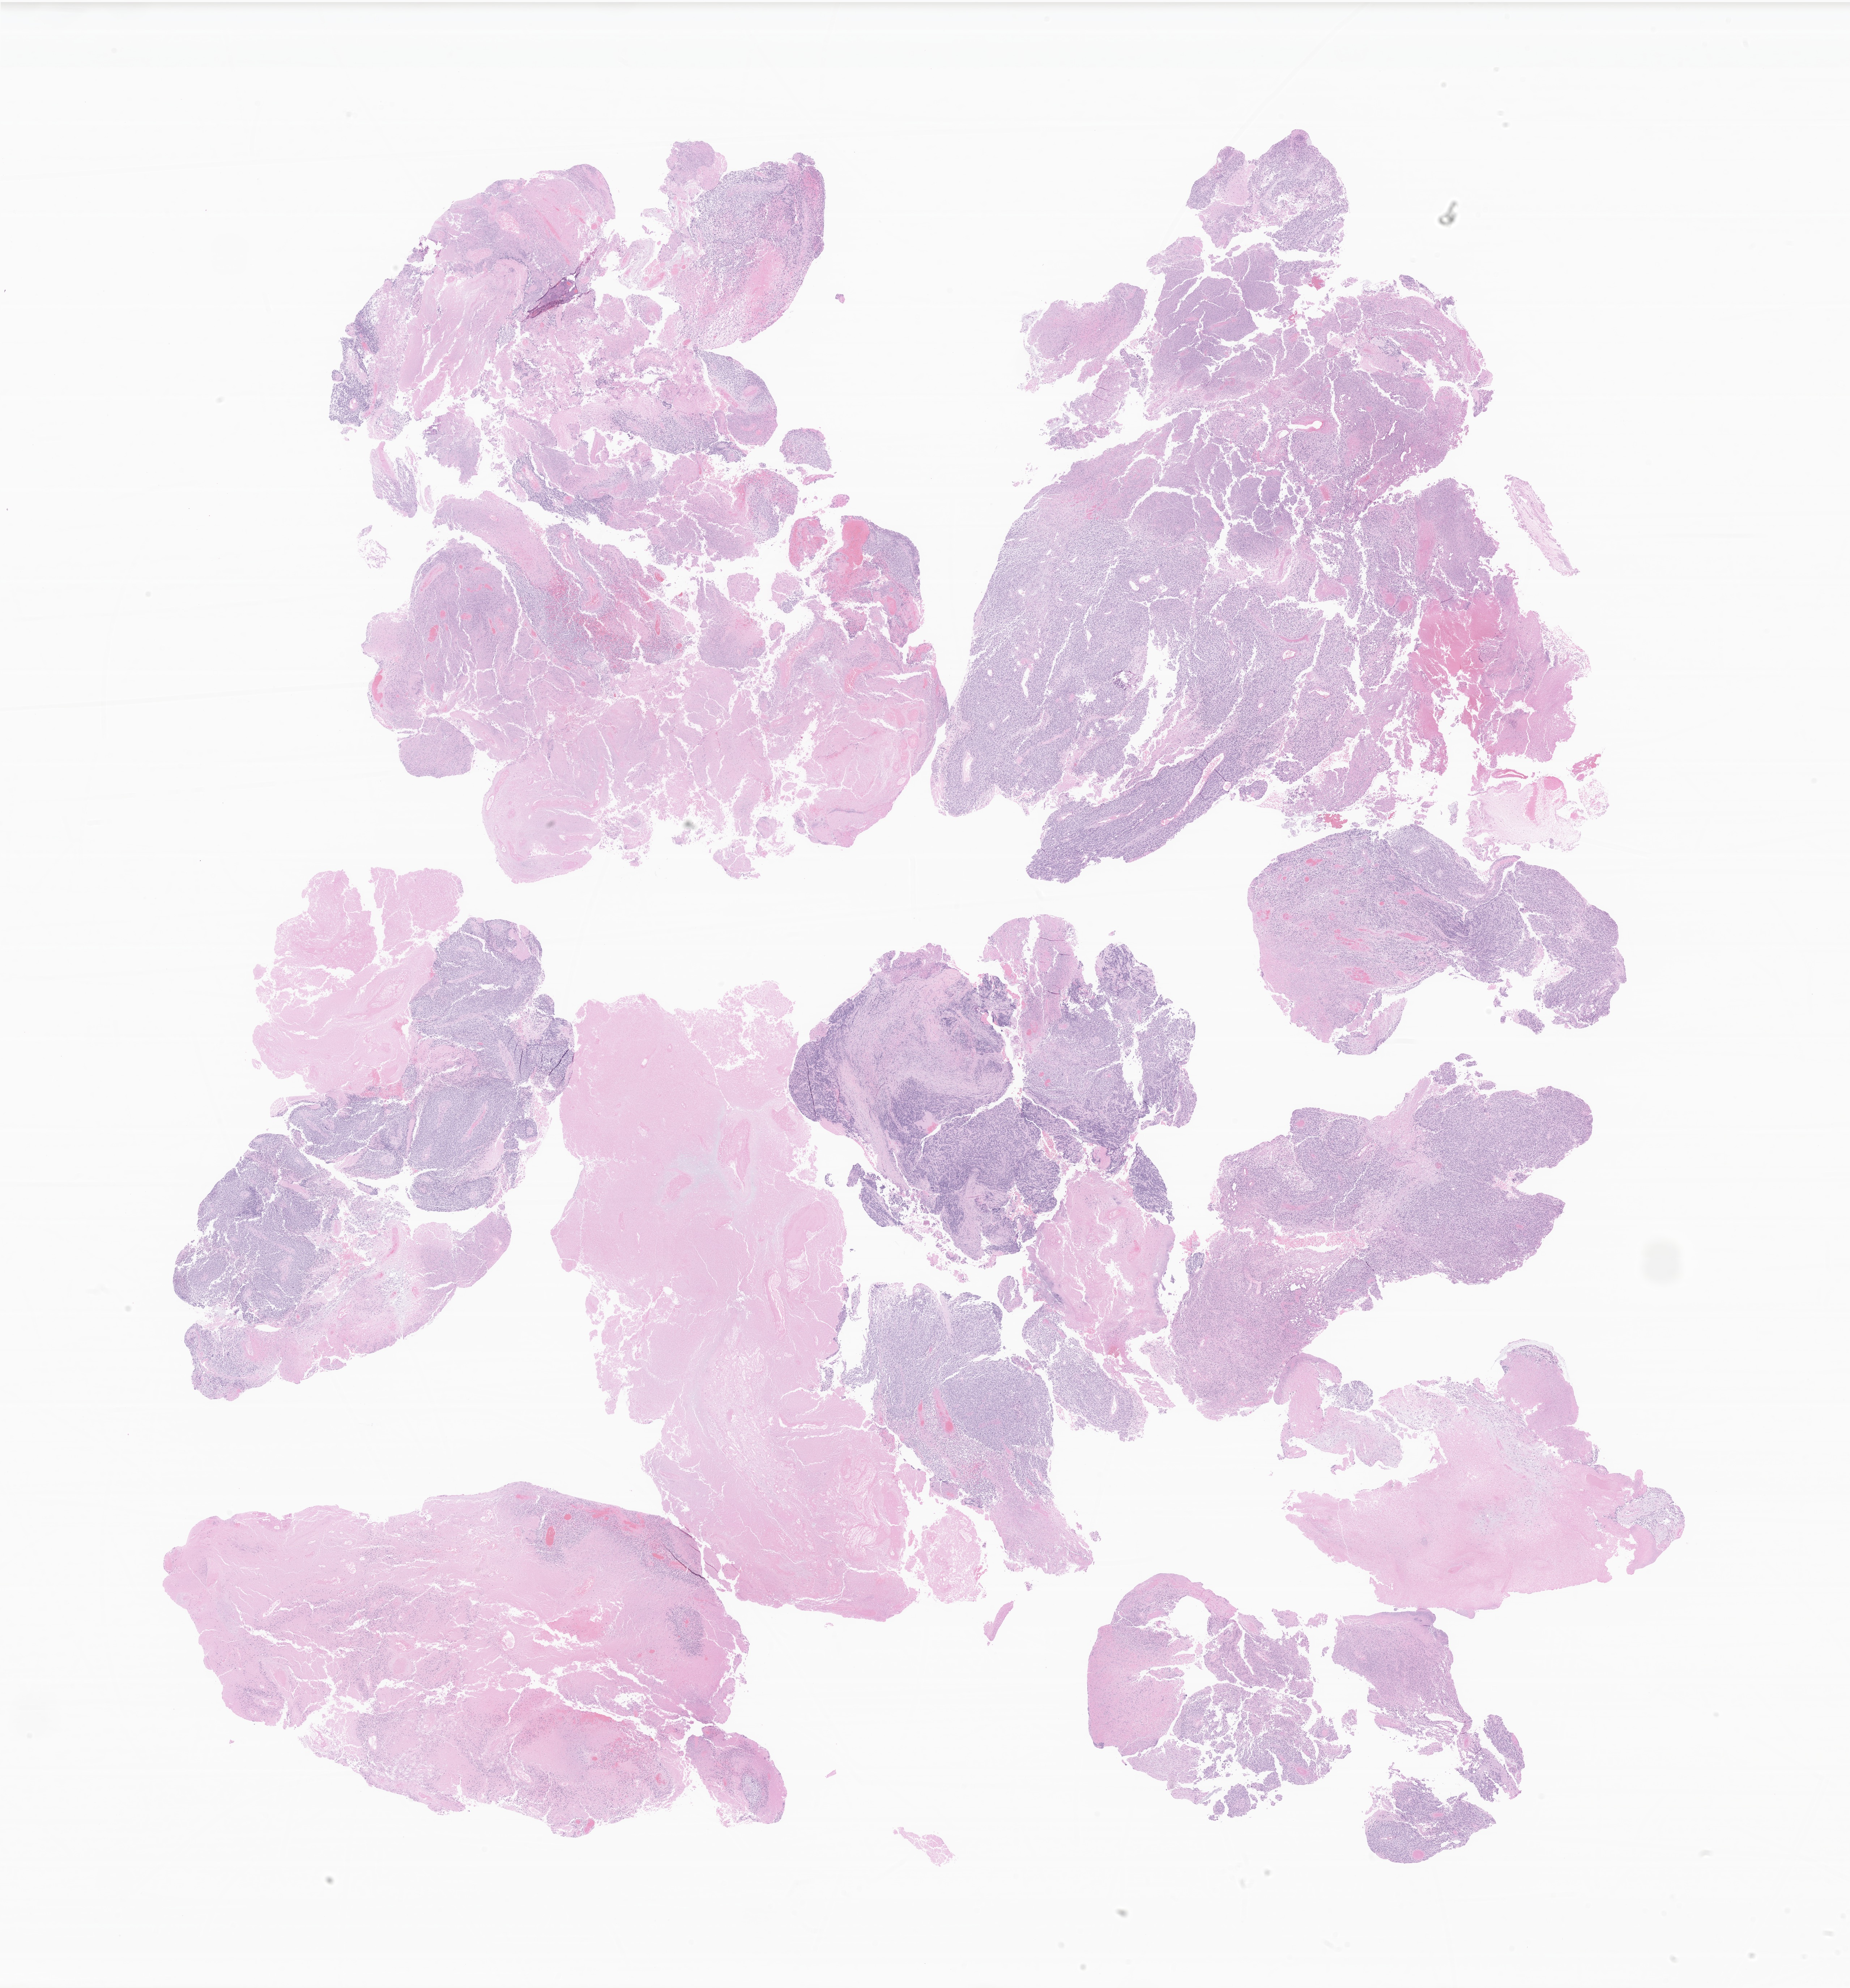
Whole-slide image, hematoxylin and eosin (H&E) stain of tumor tissue from the soft tissues of head and neck, whole scanned area (about 21.6 x 23.2 mm) shown as a low-resolution overview; FFPE section. Patient female; age 164 months (13 years 8 months).
Diagnosis (ICD-O-3 morphology term): Embryonal rhabdomyosarcoma, NOS. Tissue or organ of origin (case record): connective, subcutaneous and other soft tissues of head, face, and neck.